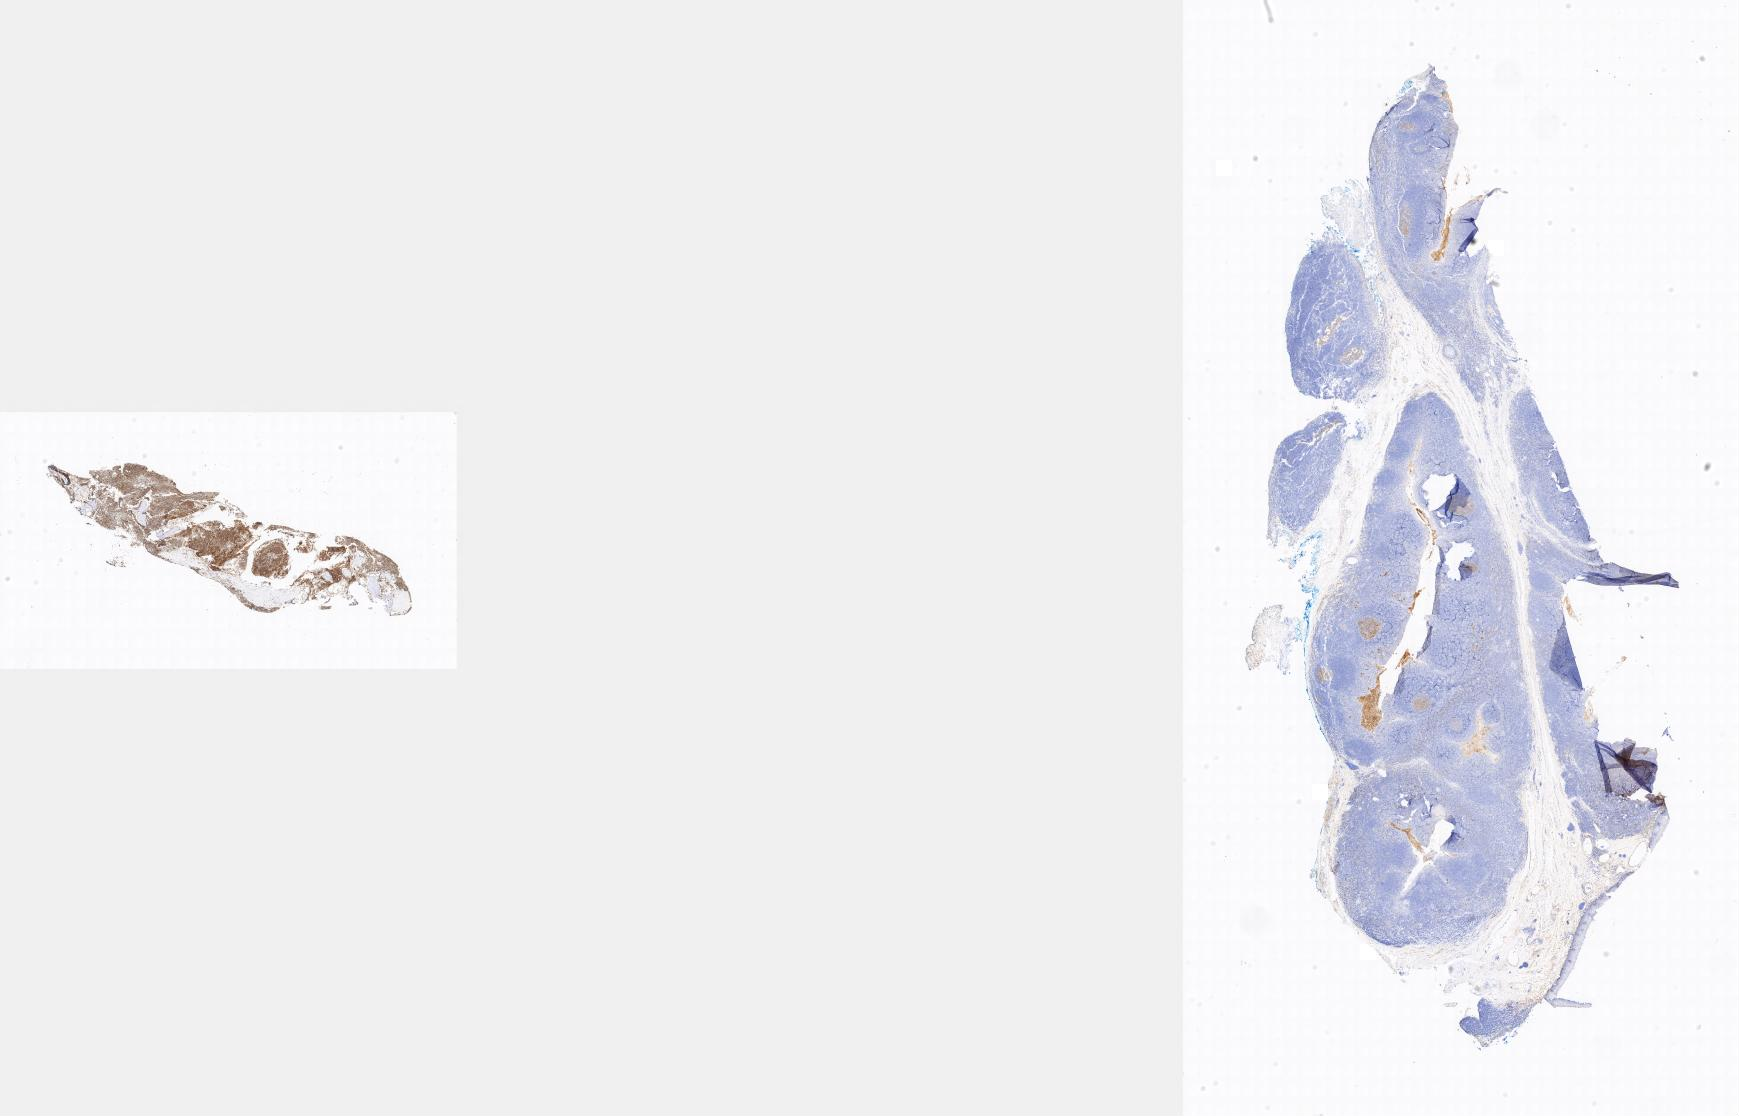
Immunohistochemistry (IHC) whole-slide image stained for CD10, a low-resolution overview of the entire scanned area. Tumor tissue. Site: bone marrow. Female patient; age at initial diagnosis 3 years.
Diagnosis: Burkitt lymphoma, NOS.